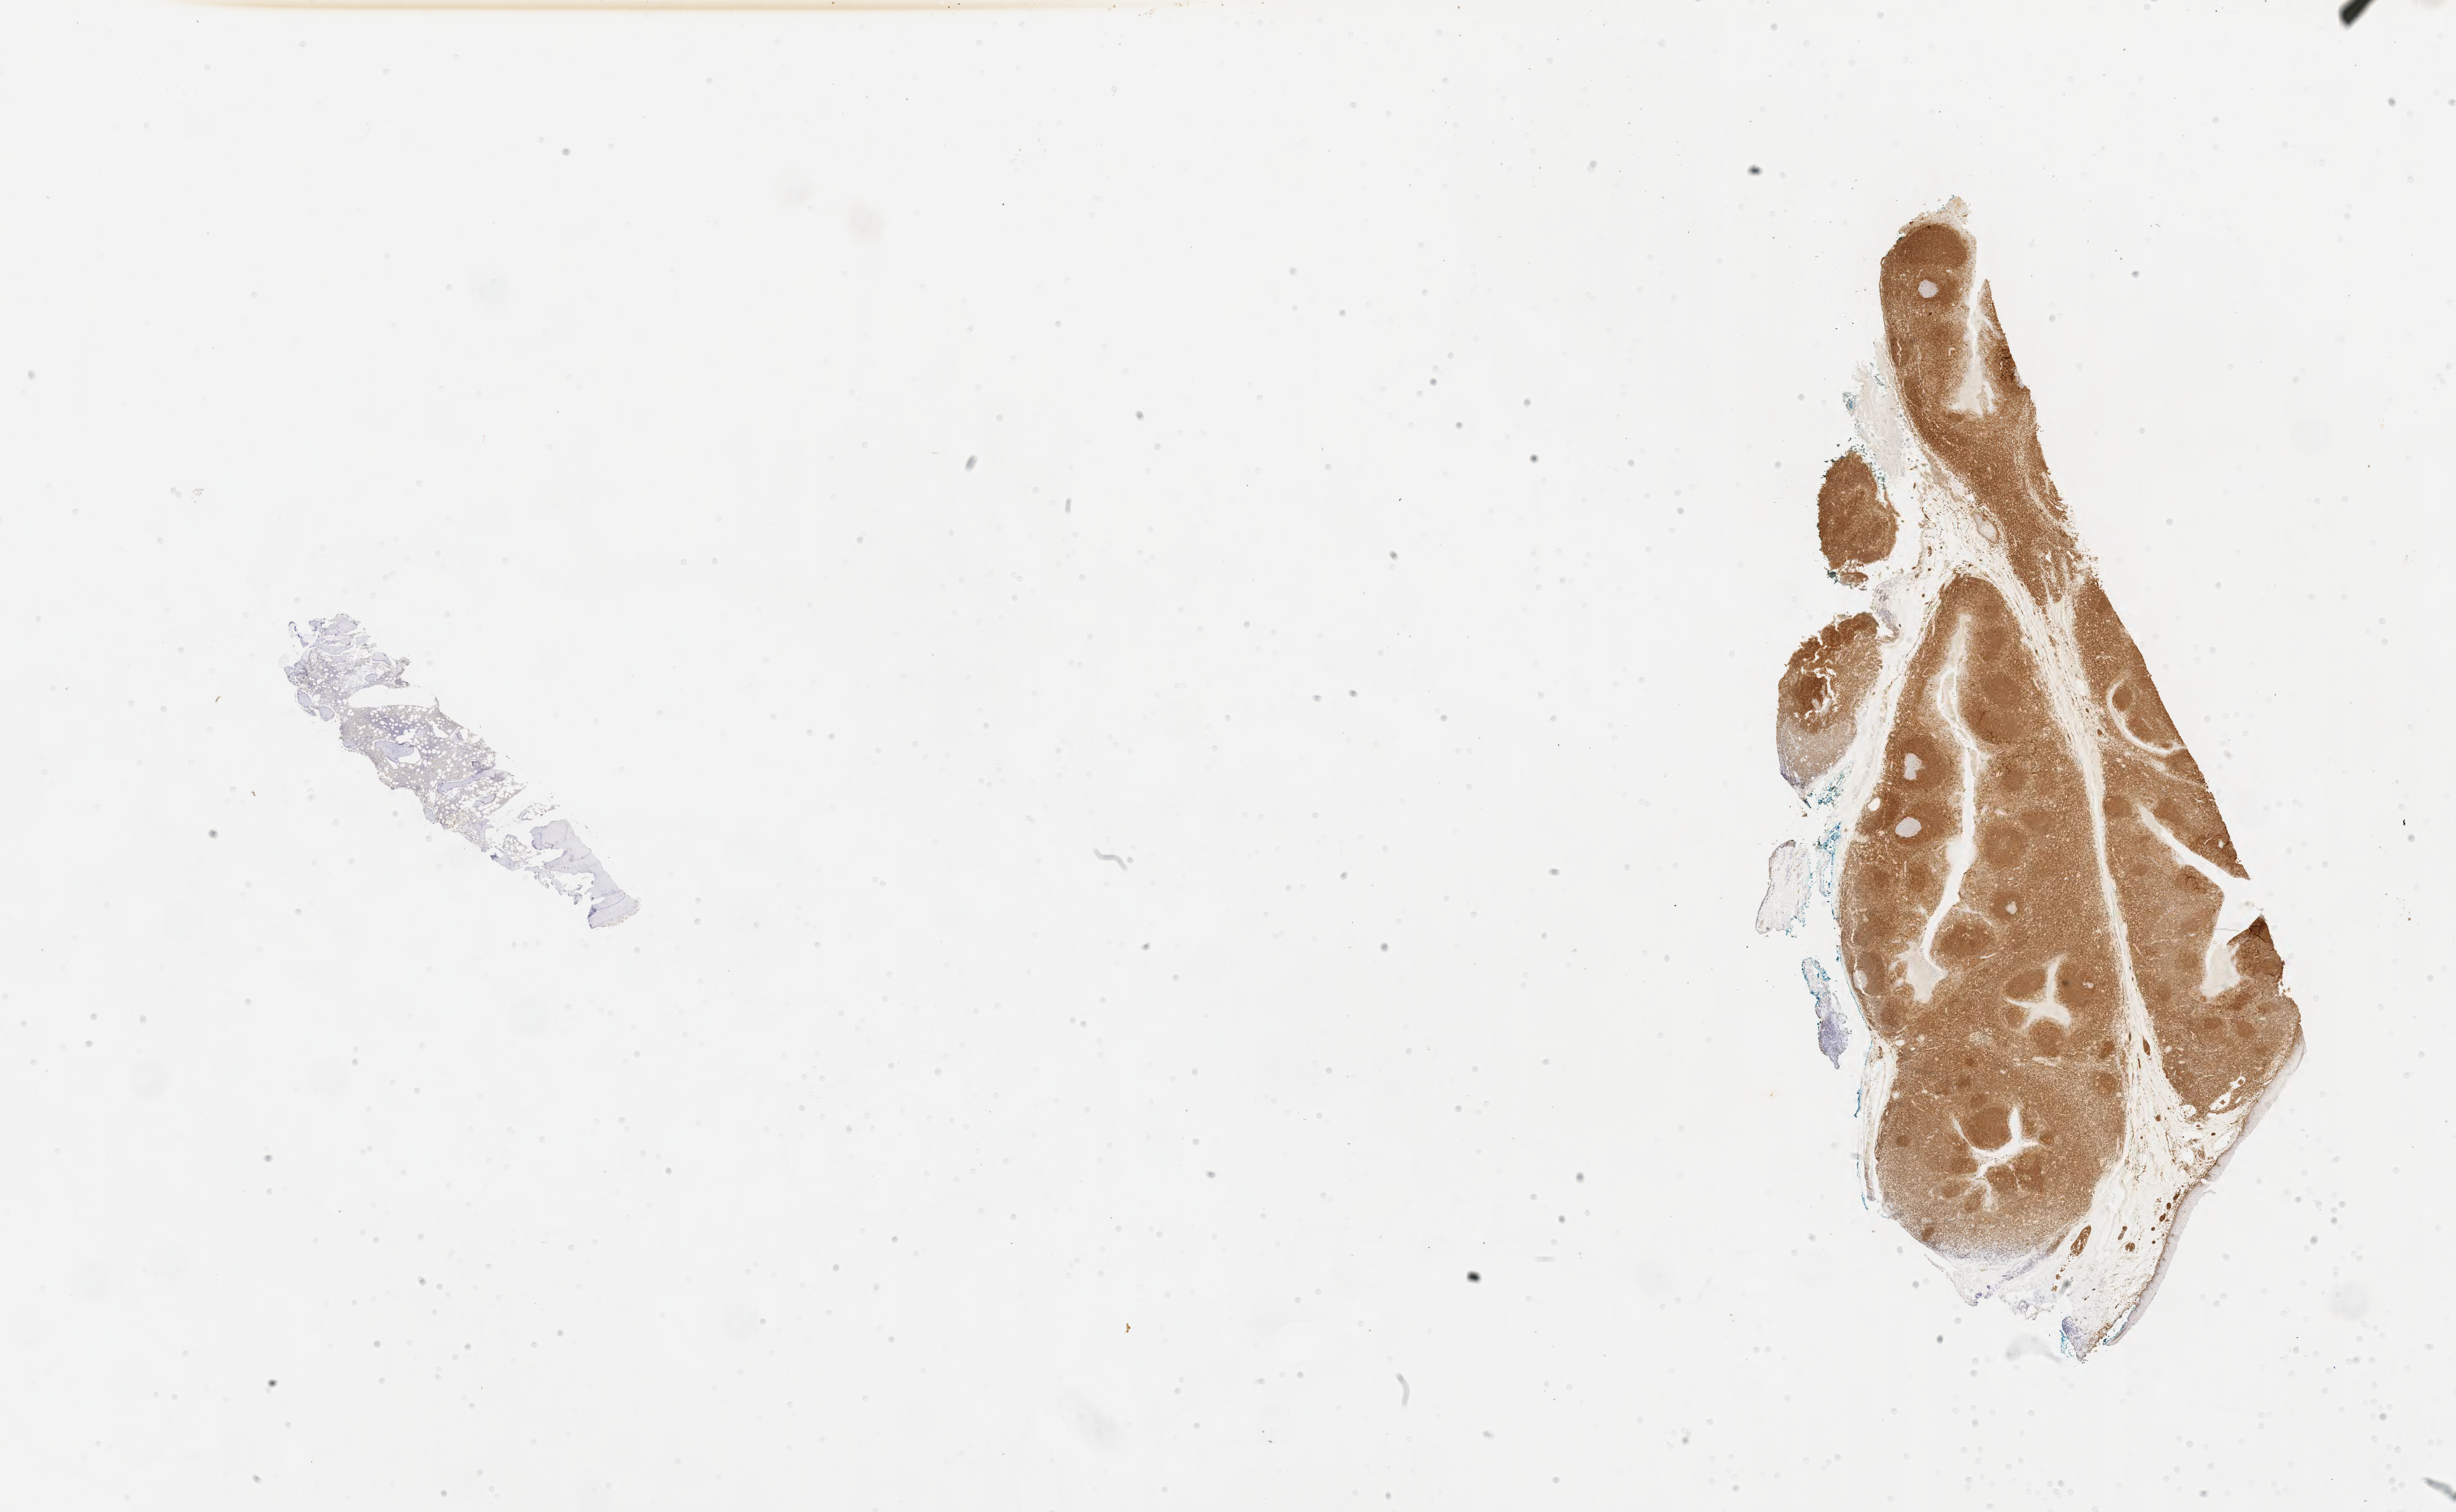
Whole-slide image, immunohistochemical stain for BCL2 — low-resolution overview of the scanned area, about 31.2 x 19.2 mm, specimen: tumor tissue, site: bone marrow. Patient: female, age at initial diagnosis 4 years.
• histologic diagnosis: Burkitt lymphoma, NOS